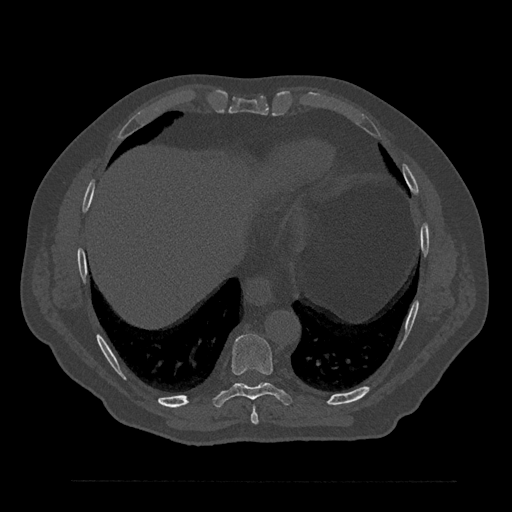
CT including the spine, one axial slice; position 404 of 797 along the scan axis; bone window (W 1800 / L 400 HU); 0.5 mm slice thickness; 512 × 512 image matrix, field of view 430 × 430 mm. Patient: male, 61 years. From the clinical record (not read from this slice): primary cancer: prostate.
Annotated regions visible in this slice (semi-automatic segmentation, software-assisted and operator-edited):
- T8 vertebra: bounding box [x1, y1, x2, y2] px = [251, 406, 259, 425]
- T9 vertebra: [212, 333, 292, 408]